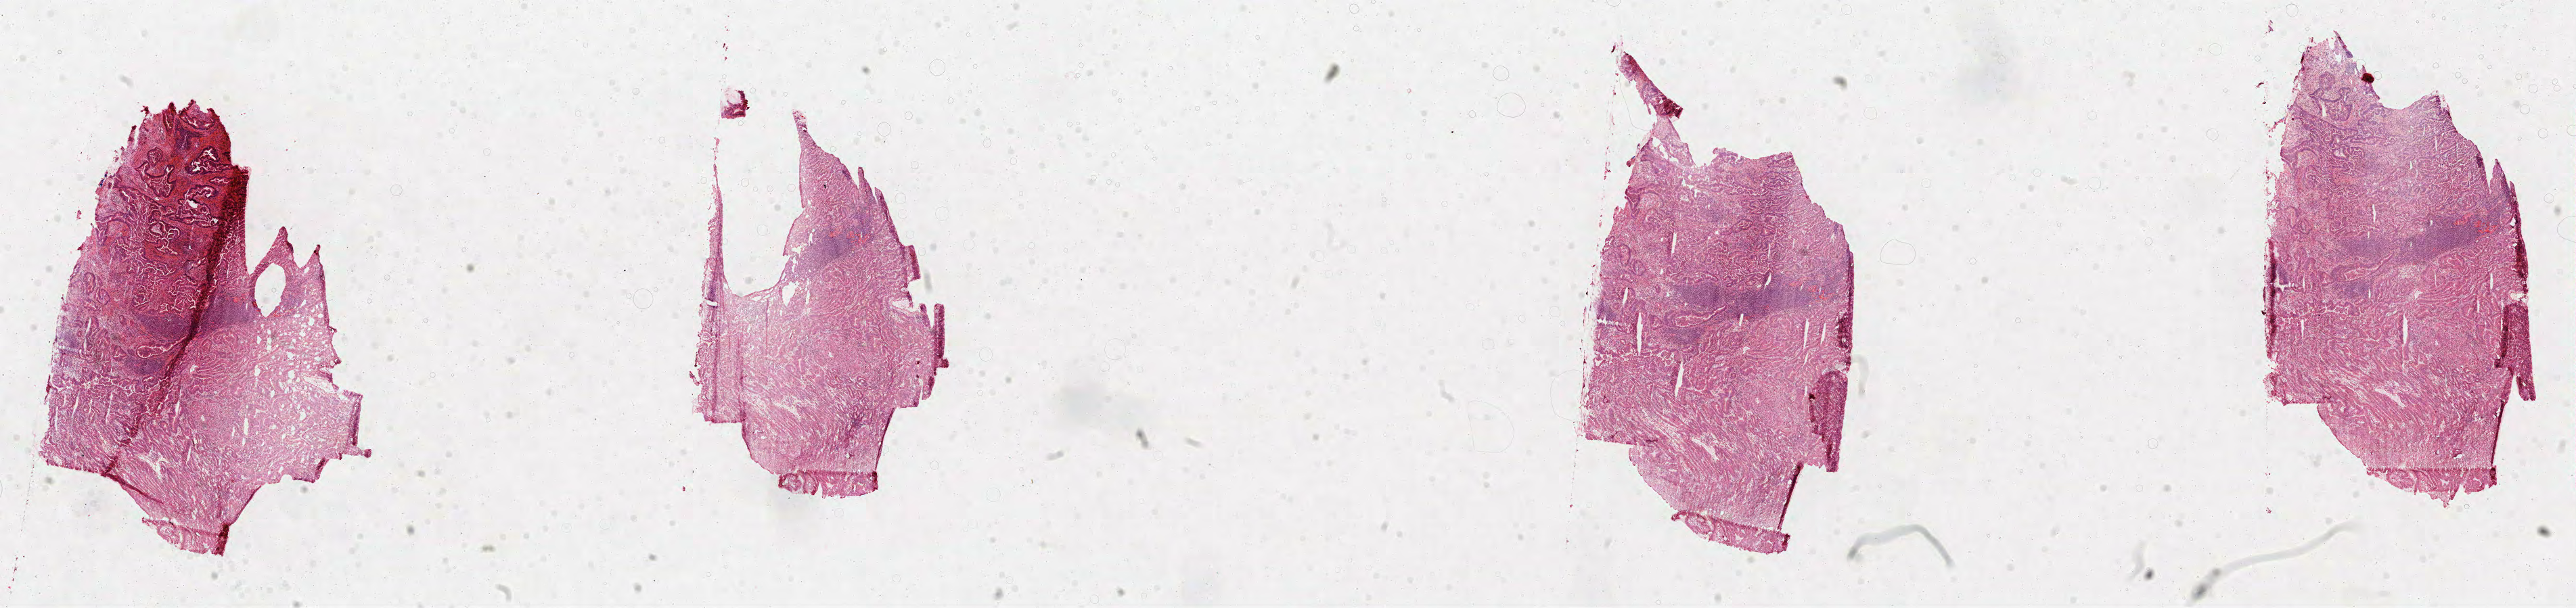
Digitized H&E tissue section (whole slide) — a low-resolution overview of the entire scanned area, about 30.7 x 7.2 mm; formalin-fixed paraffin-embedded (FFPE) diagnostic section; sample: primary tumour, stomach. Male, age 63 years at initial diagnosis. Histologic grade: G3 (poorly differentiated).
Pathologic diagnosis: Tubular adenocarcinoma. Lymph nodes positive (case pathology): 20 of 31 examined. AJCC pathologic stage: IIIA.